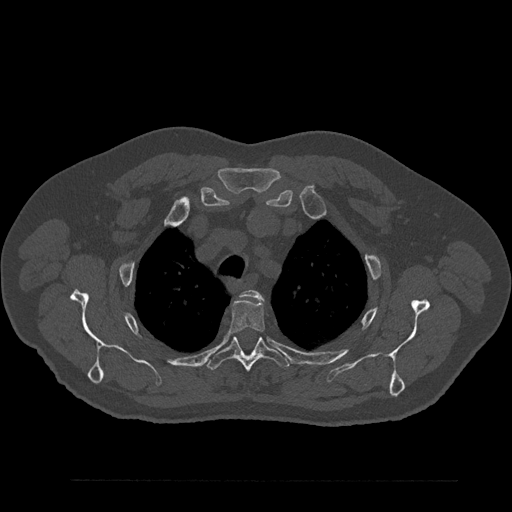
CT including the spine, one axial slice. Slice 666 of 797 in the series (ordered by position). 120 kVp. Bone window (W 1800 / L 400 HU). 0.5 mm slice thickness. 512 × 512 image matrix, field of view 430 × 430 mm. Male patient, age 61 years. From the clinical record (not read from this slice): primary cancer: prostate.
Outlined on this slice (semi-automatic segmentation, software-assisted and operator-edited):
- T2 vertebra: bounding box [x1, y1, x2, y2] px = [240, 290, 263, 300]
- T3 vertebra: [227, 298, 265, 335]
- T4 vertebra: [207, 336, 289, 372]